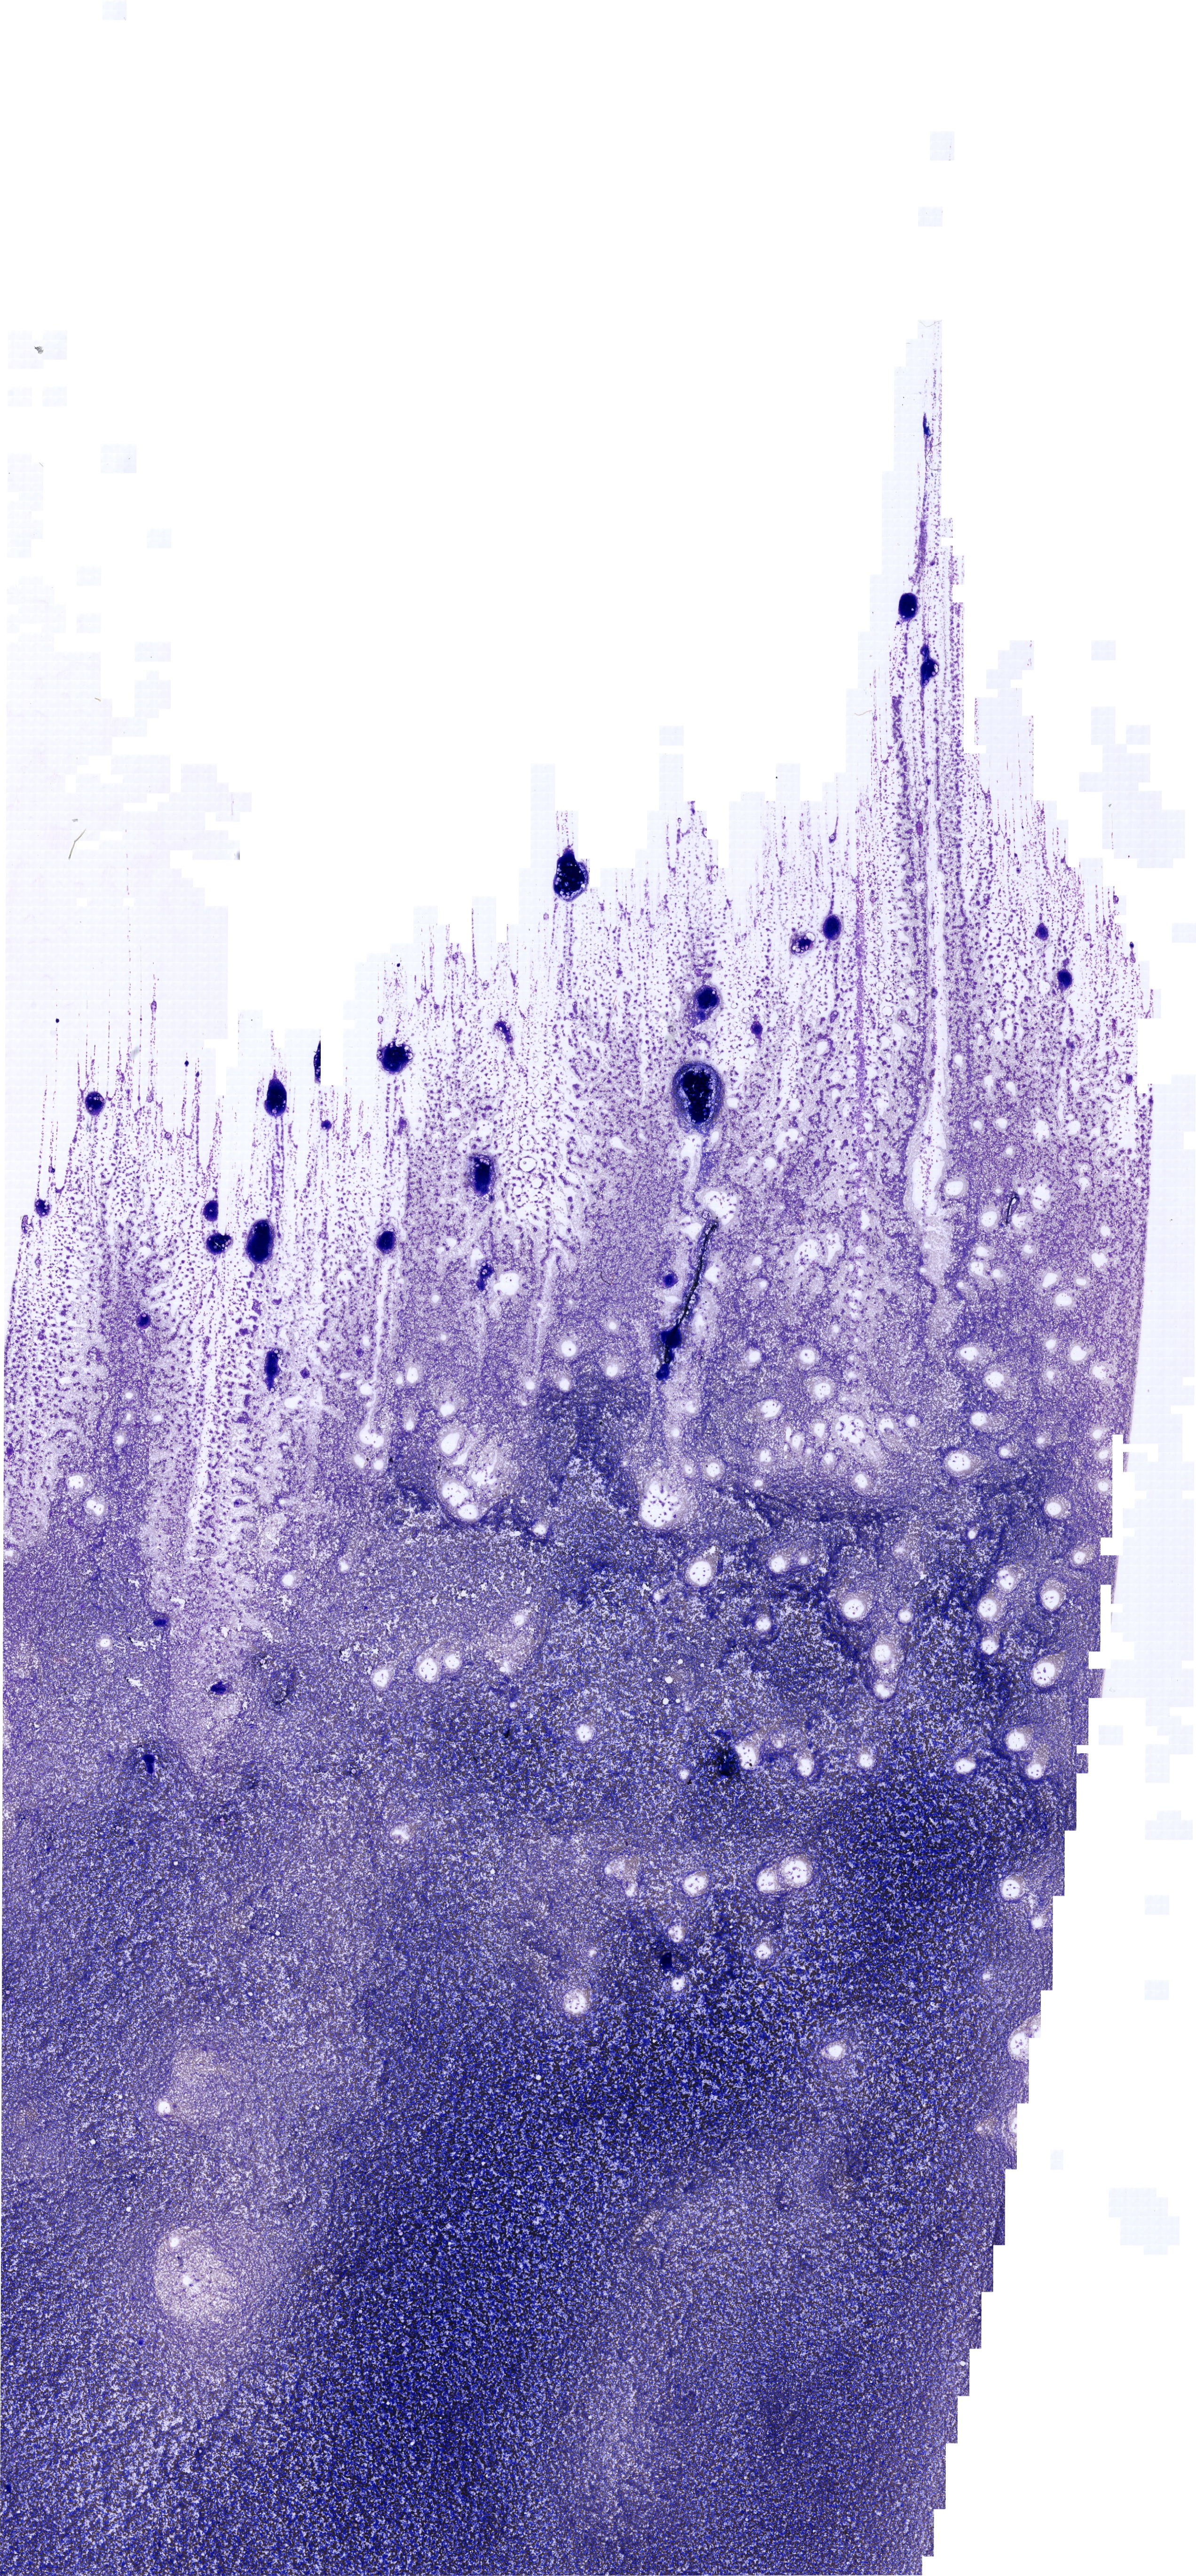
Bone marrow aspirate smear, May-Grünwald–Giemsa stain, whole-slide image — shown as a low-resolution overview of the whole scanned area (about 19.9 x 42.8 mm). Female patient.
* diagnosis: Mixed Phenotype Acute Leukemia, B/Myeloid